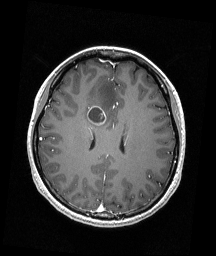
Brain MRI from a brain-tumour surgery series, one axial slice. Position 73 of 192 along the scan axis. T1-weighted post-contrast. 1 mm slice thickness. 216 × 256 image matrix. From the clinical record (not read from this slice): histopathology: Astrocytoma; WHO grade: 4.
Annotated regions visible in this slice (expert manual segmentation):
- tumour: box from (x=86, y=106) to (x=106, y=125) px